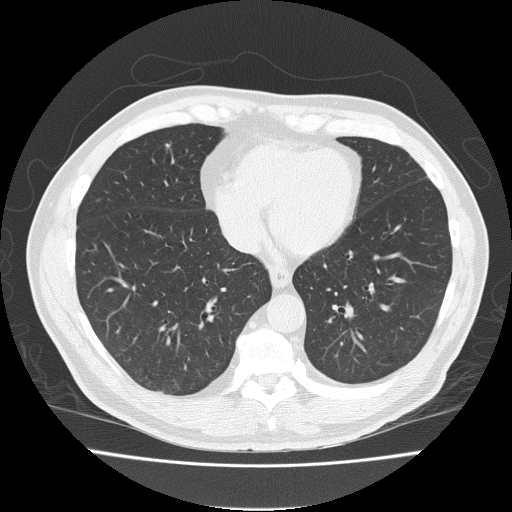
Chest CT (low-dose screening protocol), one axial image, first (baseline) screen, lung window (W 1500 / L -600 HU). Male participant, aged 57 years at enrolment. Current smoker at enrolment.
Expert reader's lesion annotation, bounding box (x1, y1, x2, y2) in pixels: (148, 135, 183, 160). Screening reader's record for this exam (one nodule recorded; not confirmed to be the boxed lesion): non-calcified nodule or mass ≥4 mm, right middle lobe, 4 × 4 mm, spiculated (stellate) margins, soft tissue attenuation. Official screen result: positive, change unspecified: nodule(s) >= 4 mm or enlarging nodule(s), mass(es), or other non-specific abnormalities suspicious for lung cancer. Participant outcome: lung cancer diagnosed 459 days after this screen — adenocarcinoma, NOS, right middle lobe, moderately differentiated (G2), stage IA (AJCC 6th edition), 12 mm at pathology.